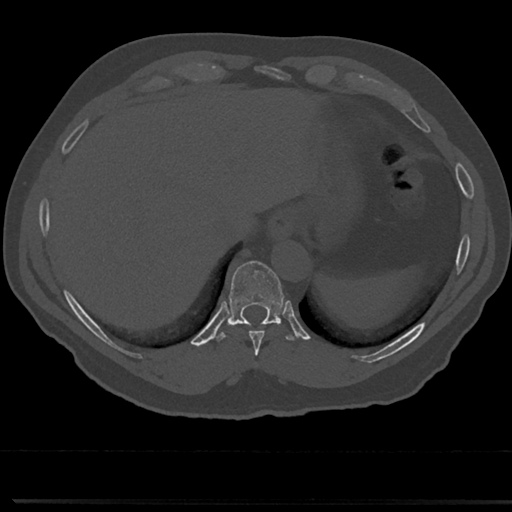
CT including the spine, one axial slice; slice 275 of 817 in the series (ordered by position); reconstruction kernel Br40s/3; bone window (W 1800 / L 400 HU); 0.5 mm slice thickness; 512 × 512 image matrix, field of view 355 × 355 mm. Male patient, age 61 years. Case-level facts recorded for this patient, not image findings: primary cancer: prostate.
Structures marked on this image (semi-automatically segmented with operator editing):
- T10 vertebra: bounding box <230,261,283,323> (left, top, right, bottom; pixels)
- T8 vertebra: <237,302,281,368>
- T9 vertebra: <228,291,286,349>